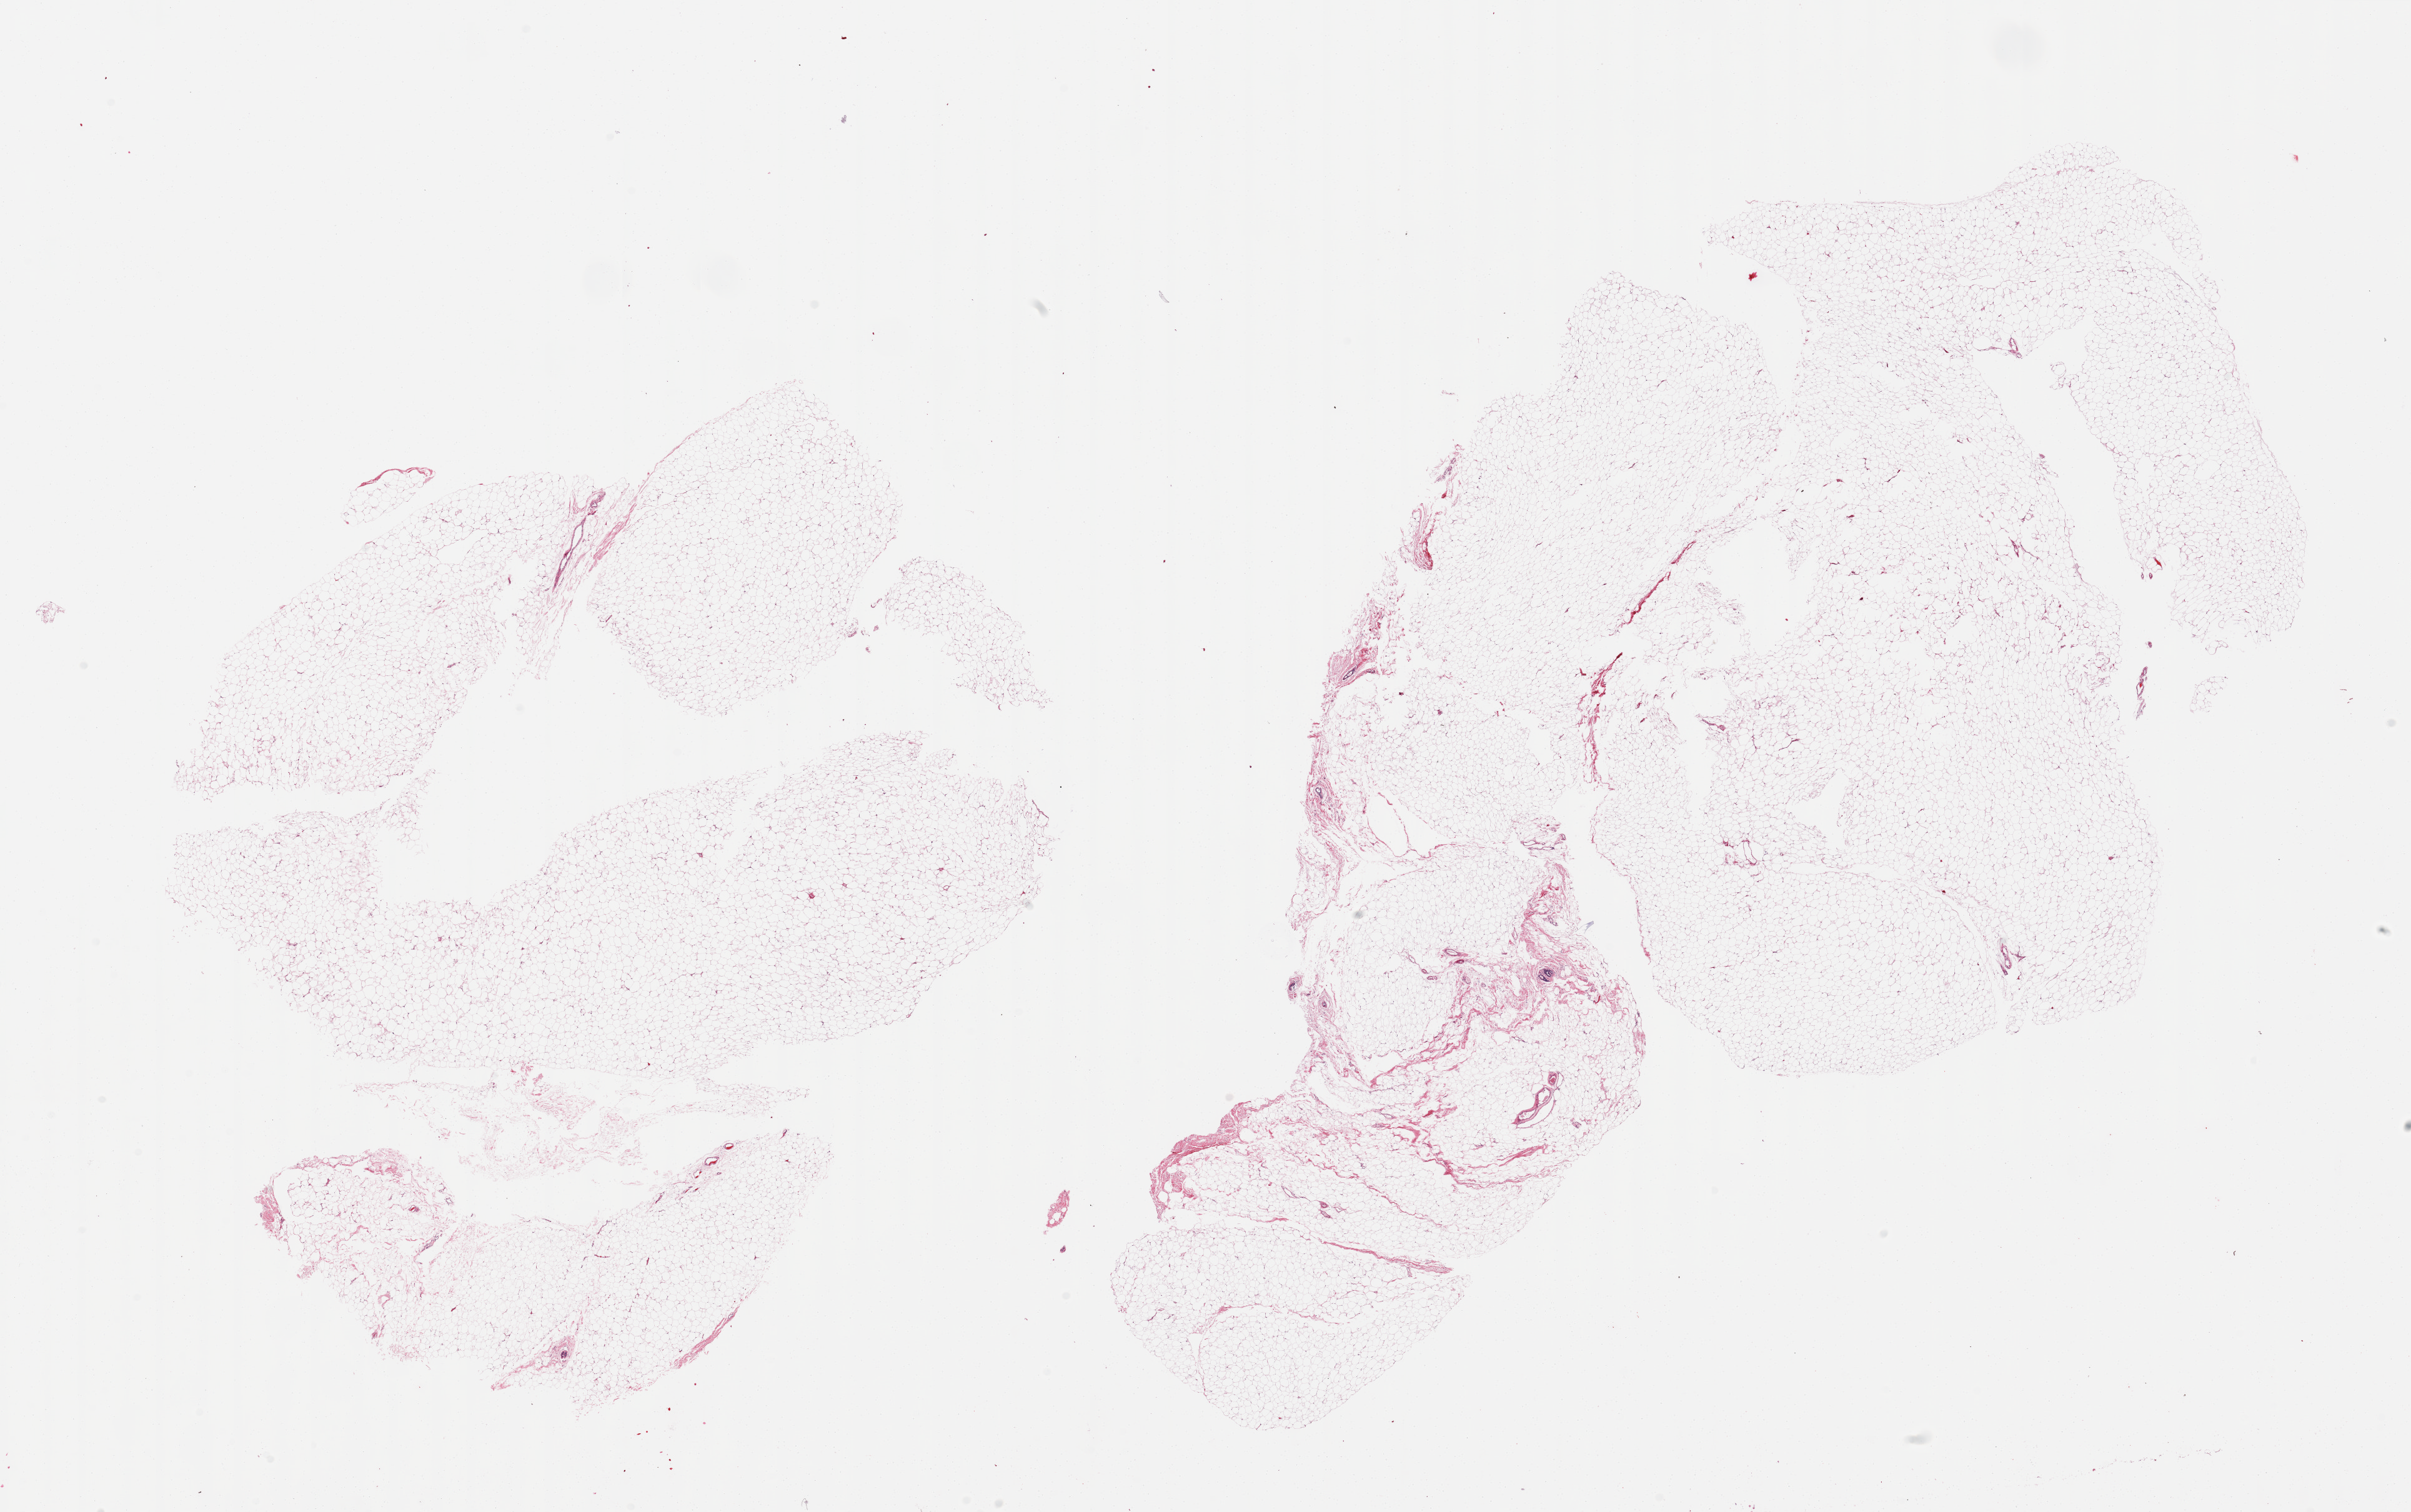
Digitized haematoxylin and eosin-stained section, brightfield, low-resolution overview of the scanned area, about 30.5 x 19.1 mm (from a 20x scan). PAXgene-fixed, paraffin-embedded tissue. Sampled site (target tissue): breast. Tissue donor sample. Female donor.
* review note (as recorded): 2 pieces, mainly adipose/fibrous elements; trace ductal elements